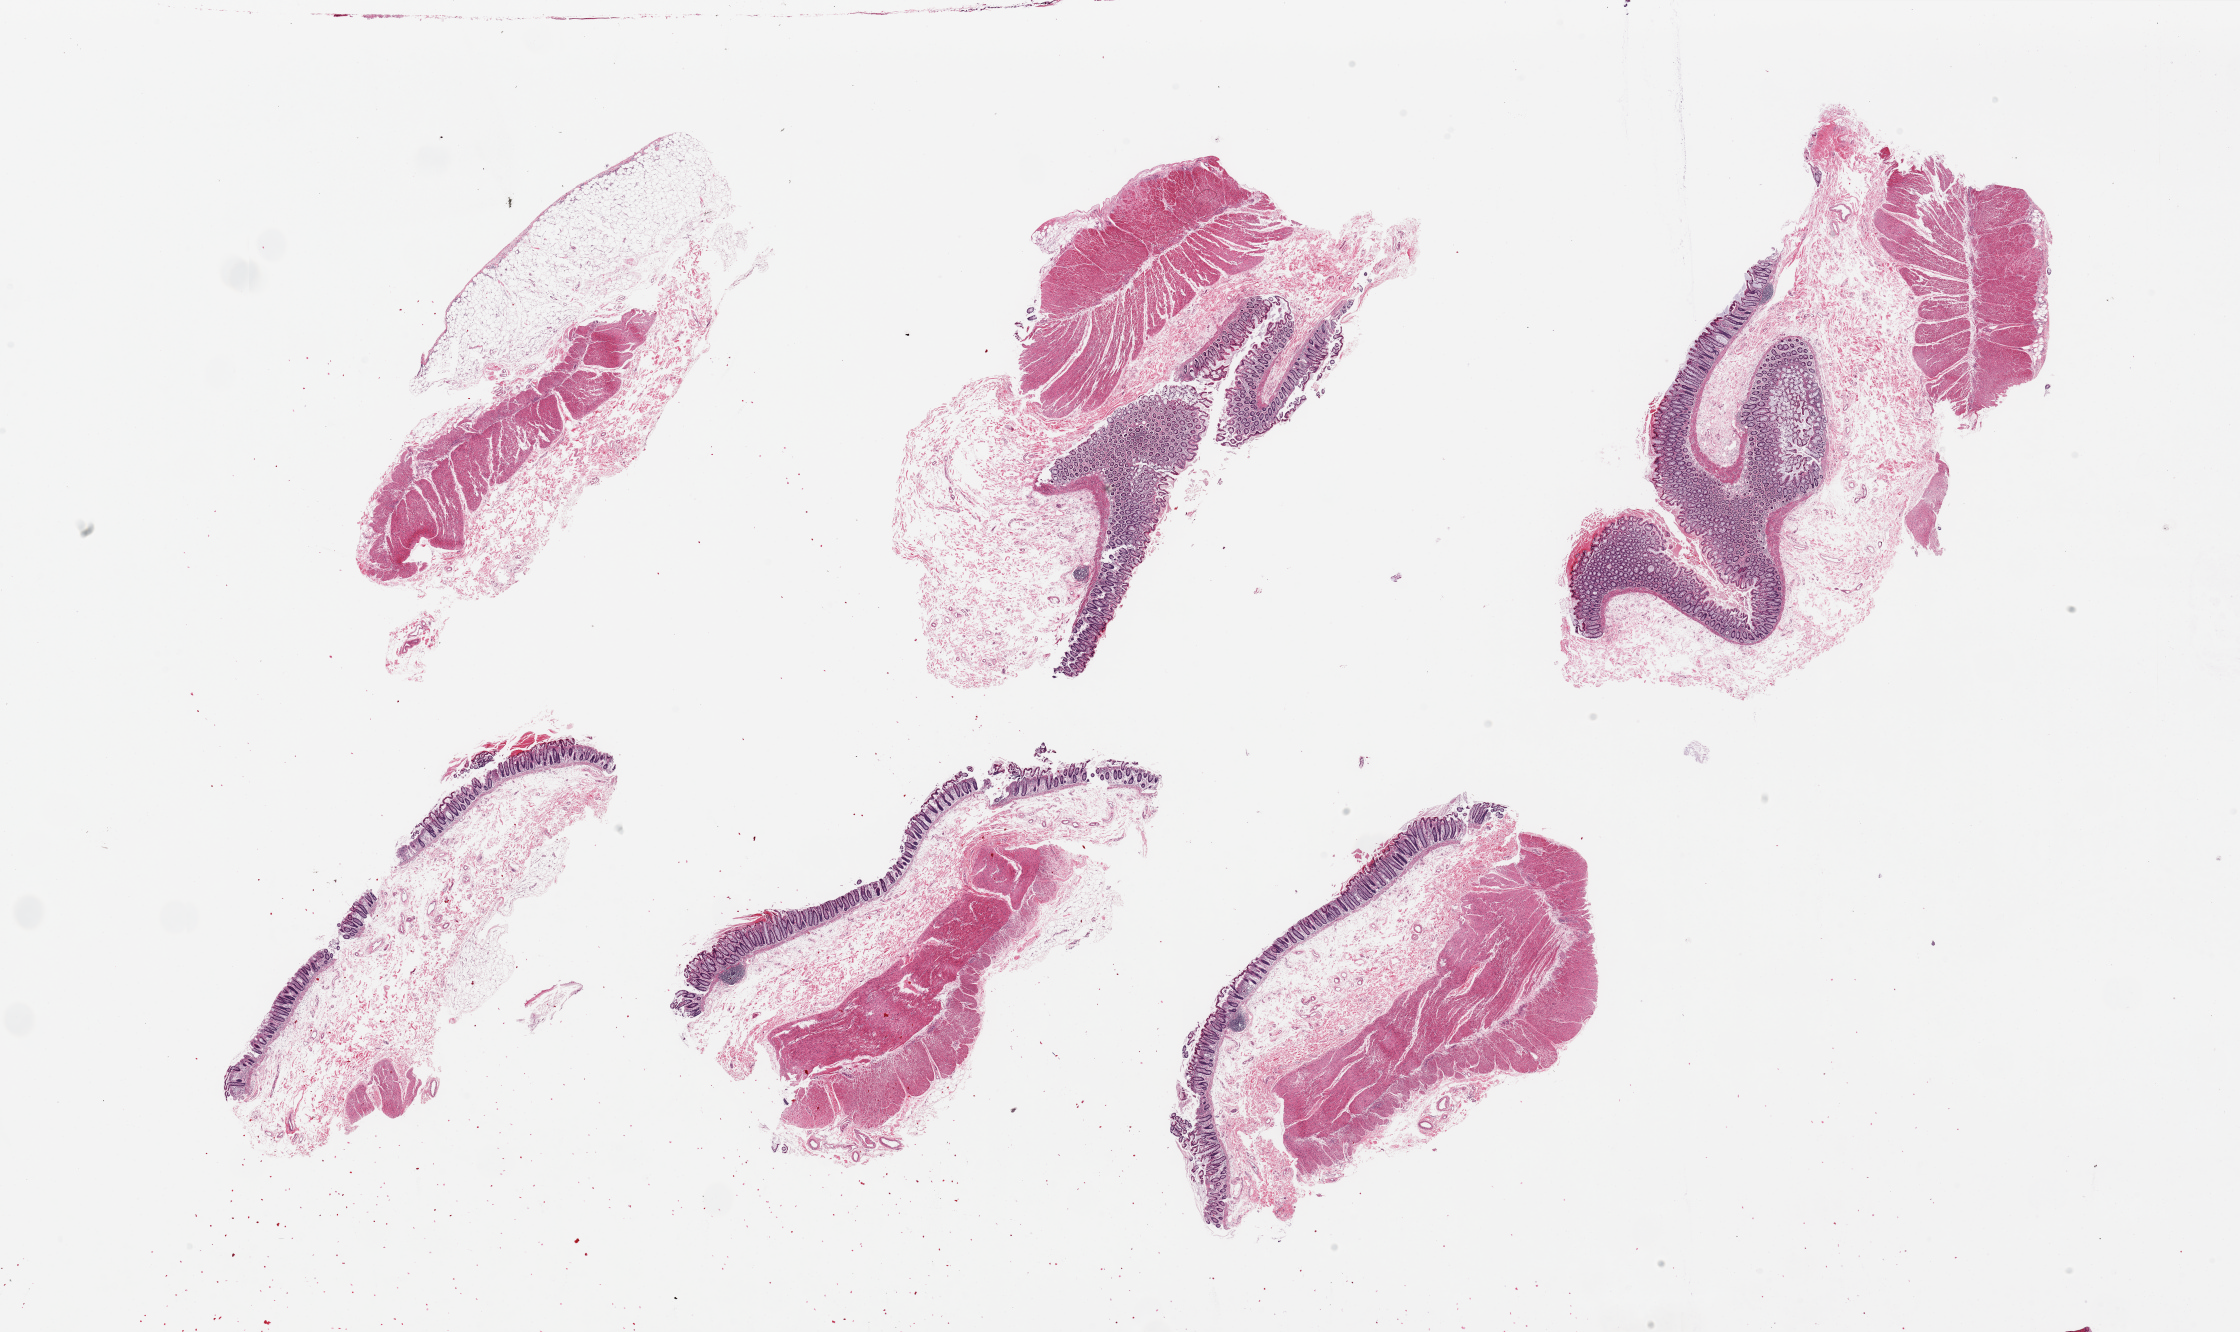
Haematoxylin and eosin whole-slide image, brightfield, shown as a low-resolution overview of the whole scanned area (about 35.4 x 21.1 mm); PAXgene-fixed paraffin-embedded (PFPE) section; section of transverse colon (target tissue); tissue donor sample. Donor: female.
• reviewer comment on this tissue sample: 6 pieces, up to 10x5.5mm; 5 have mucosa